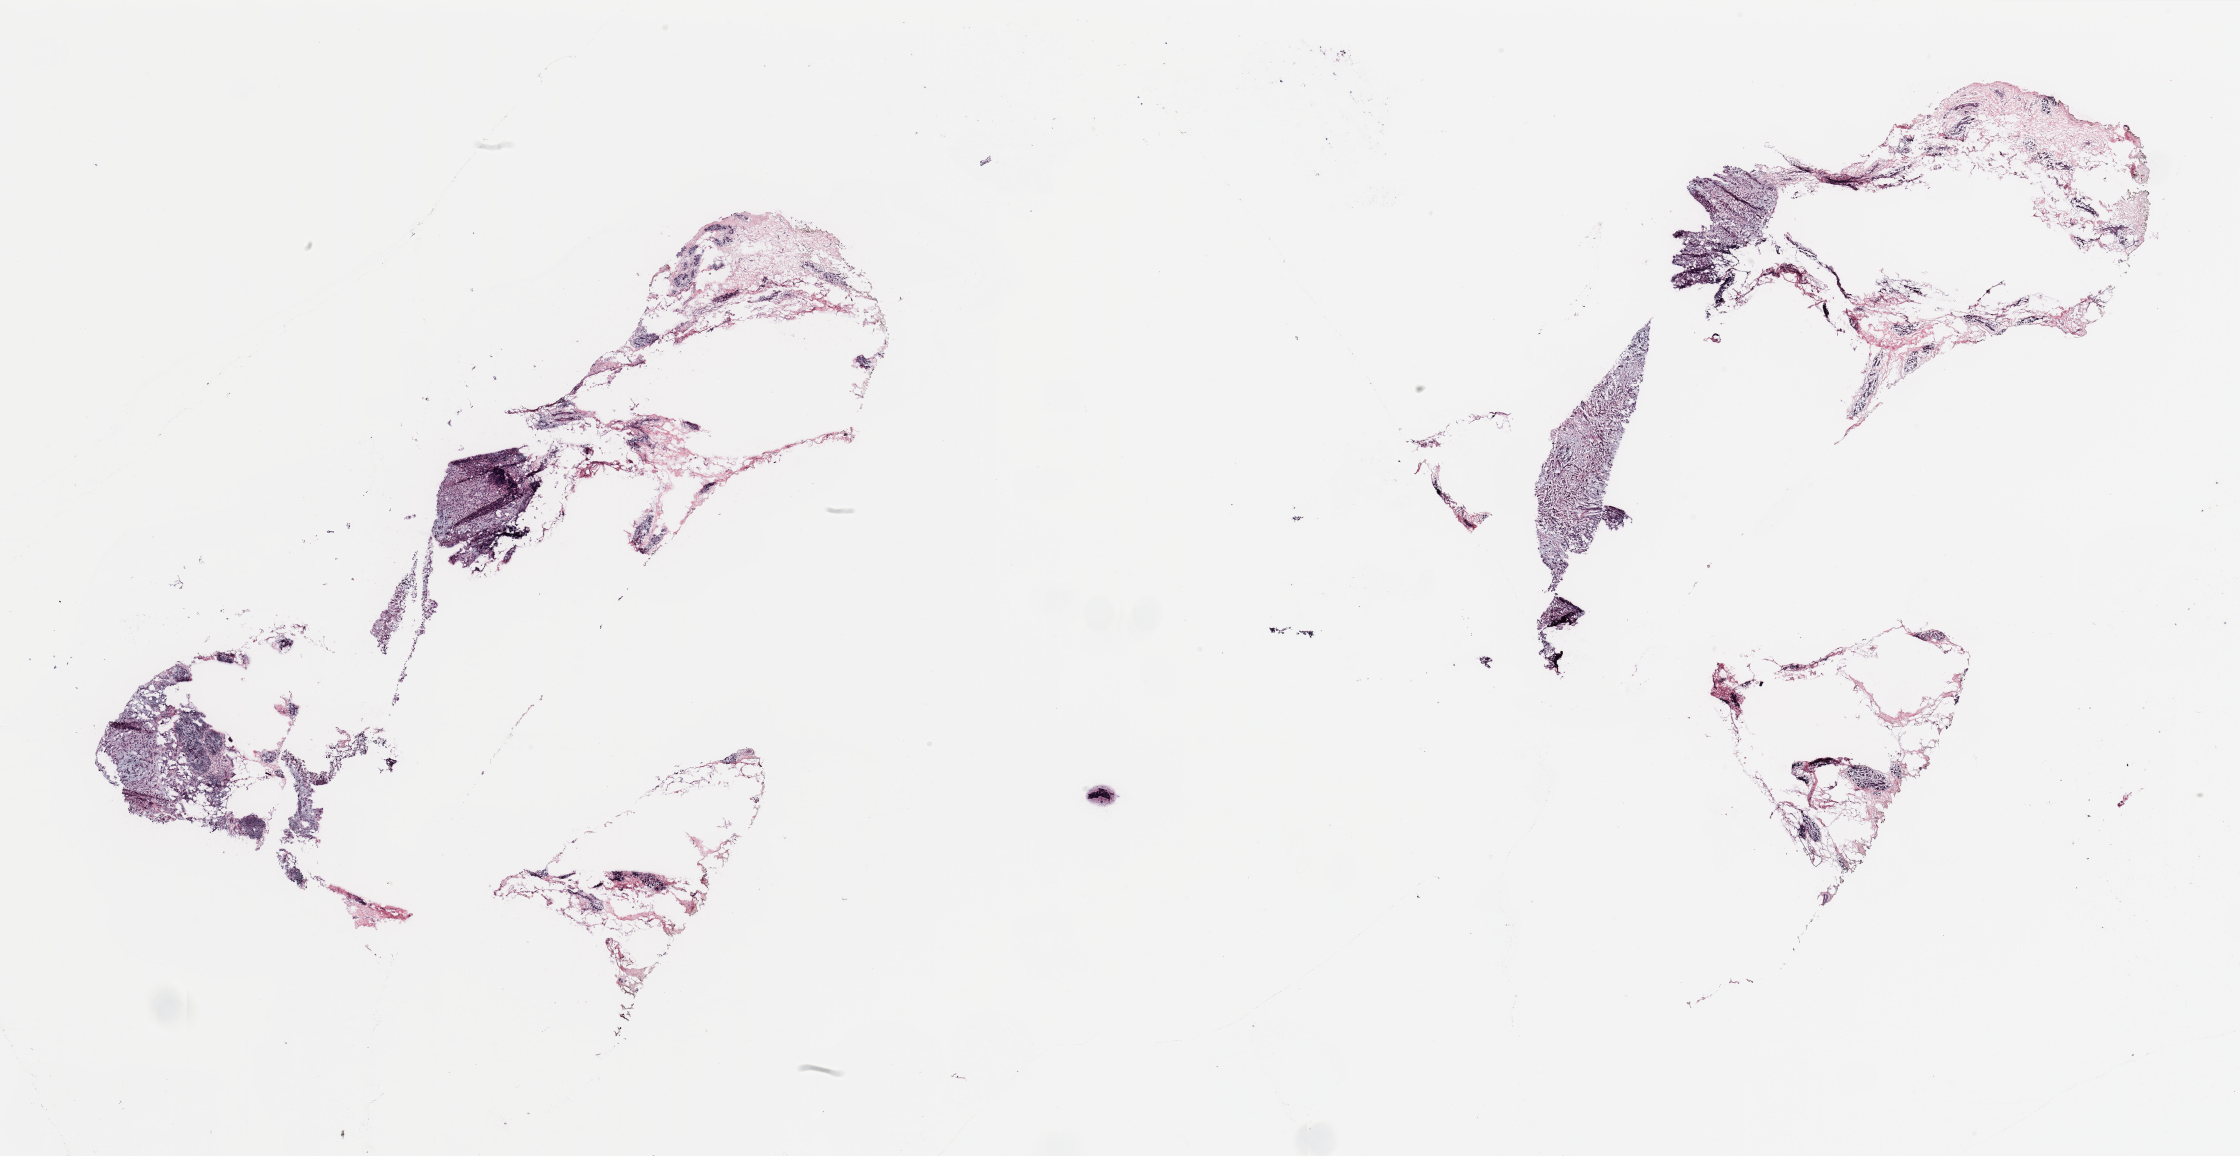
Hematoxylin and eosin (H&E) stained whole-slide image — low-resolution overview of the scanned area, about 35.4 x 18.3 mm. Breast, tumour tissue. Patient: female, age 58 years.
AJCC pathologic stage: IIA. Histologic diagnosis: Infiltrating duct carcinoma, NOS.